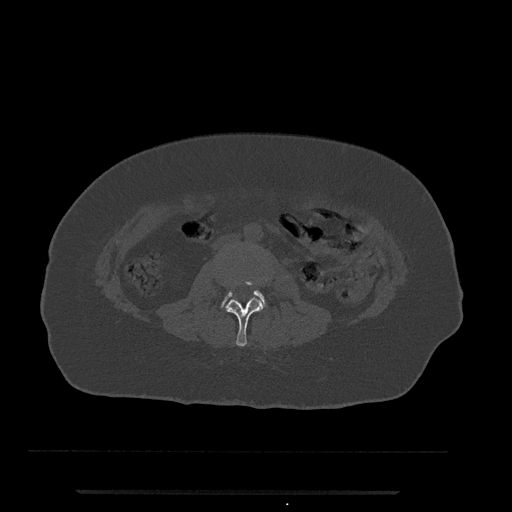
CT including the spine, one axial slice; slice 8 of 797 in the series (ordered by position); bone window (W 1800 / L 400 HU); 0.5 mm slice thickness; 512 × 512 image matrix. Patient: female, 51 years. From the clinical record (not read from this slice): primary cancer: neuro; vertebrae with lytic lesions (as recorded): T8.
Structures marked on this image (semi-automatic segmentation, software-assisted and operator-edited):
- L2 vertebra: bounding box (x1, y1, x2, y2) in pixels: (226, 278, 268, 347)